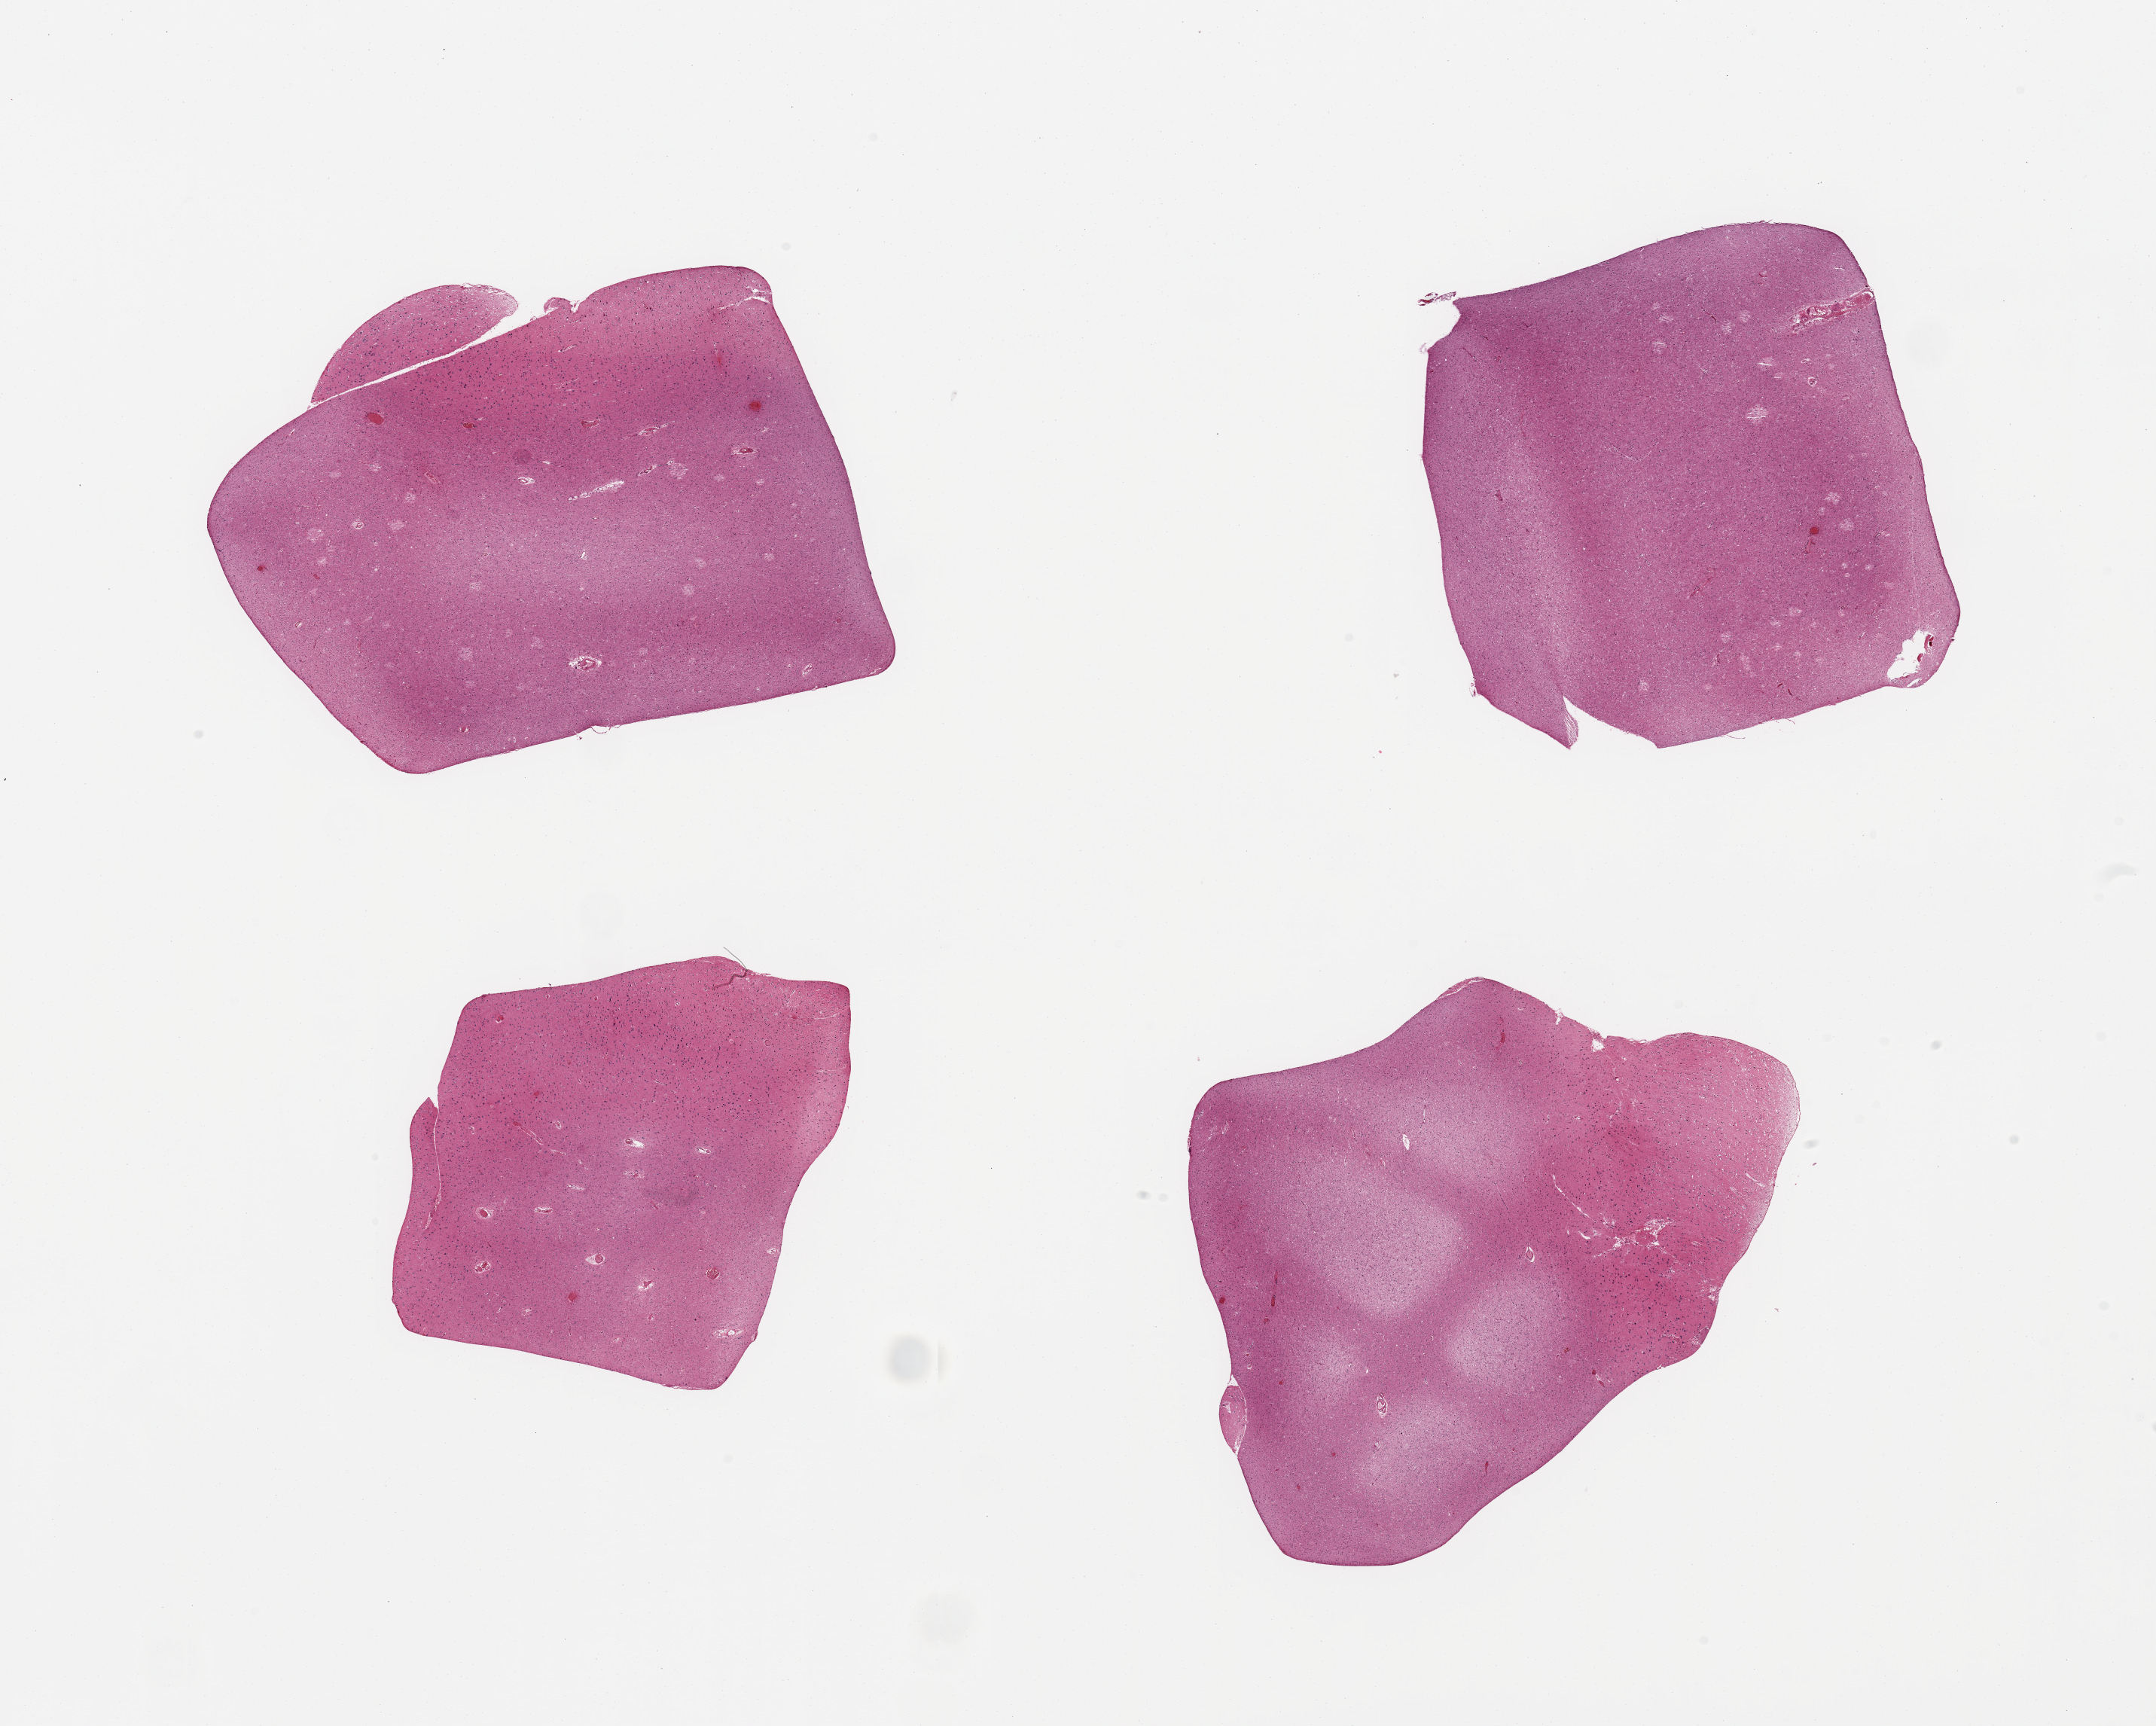
Haematoxylin and eosin whole-slide image, brightfield — shown as a low-resolution overview of the whole scanned area (about 22.6 x 18.1 mm). PAXgene-fixed, paraffin-embedded tissue. Sampled site (target tissue): cerebral cortex. Tissue donor sample. Donor sex: male.
• review note (as recorded): 4 pieces; excessive white matter